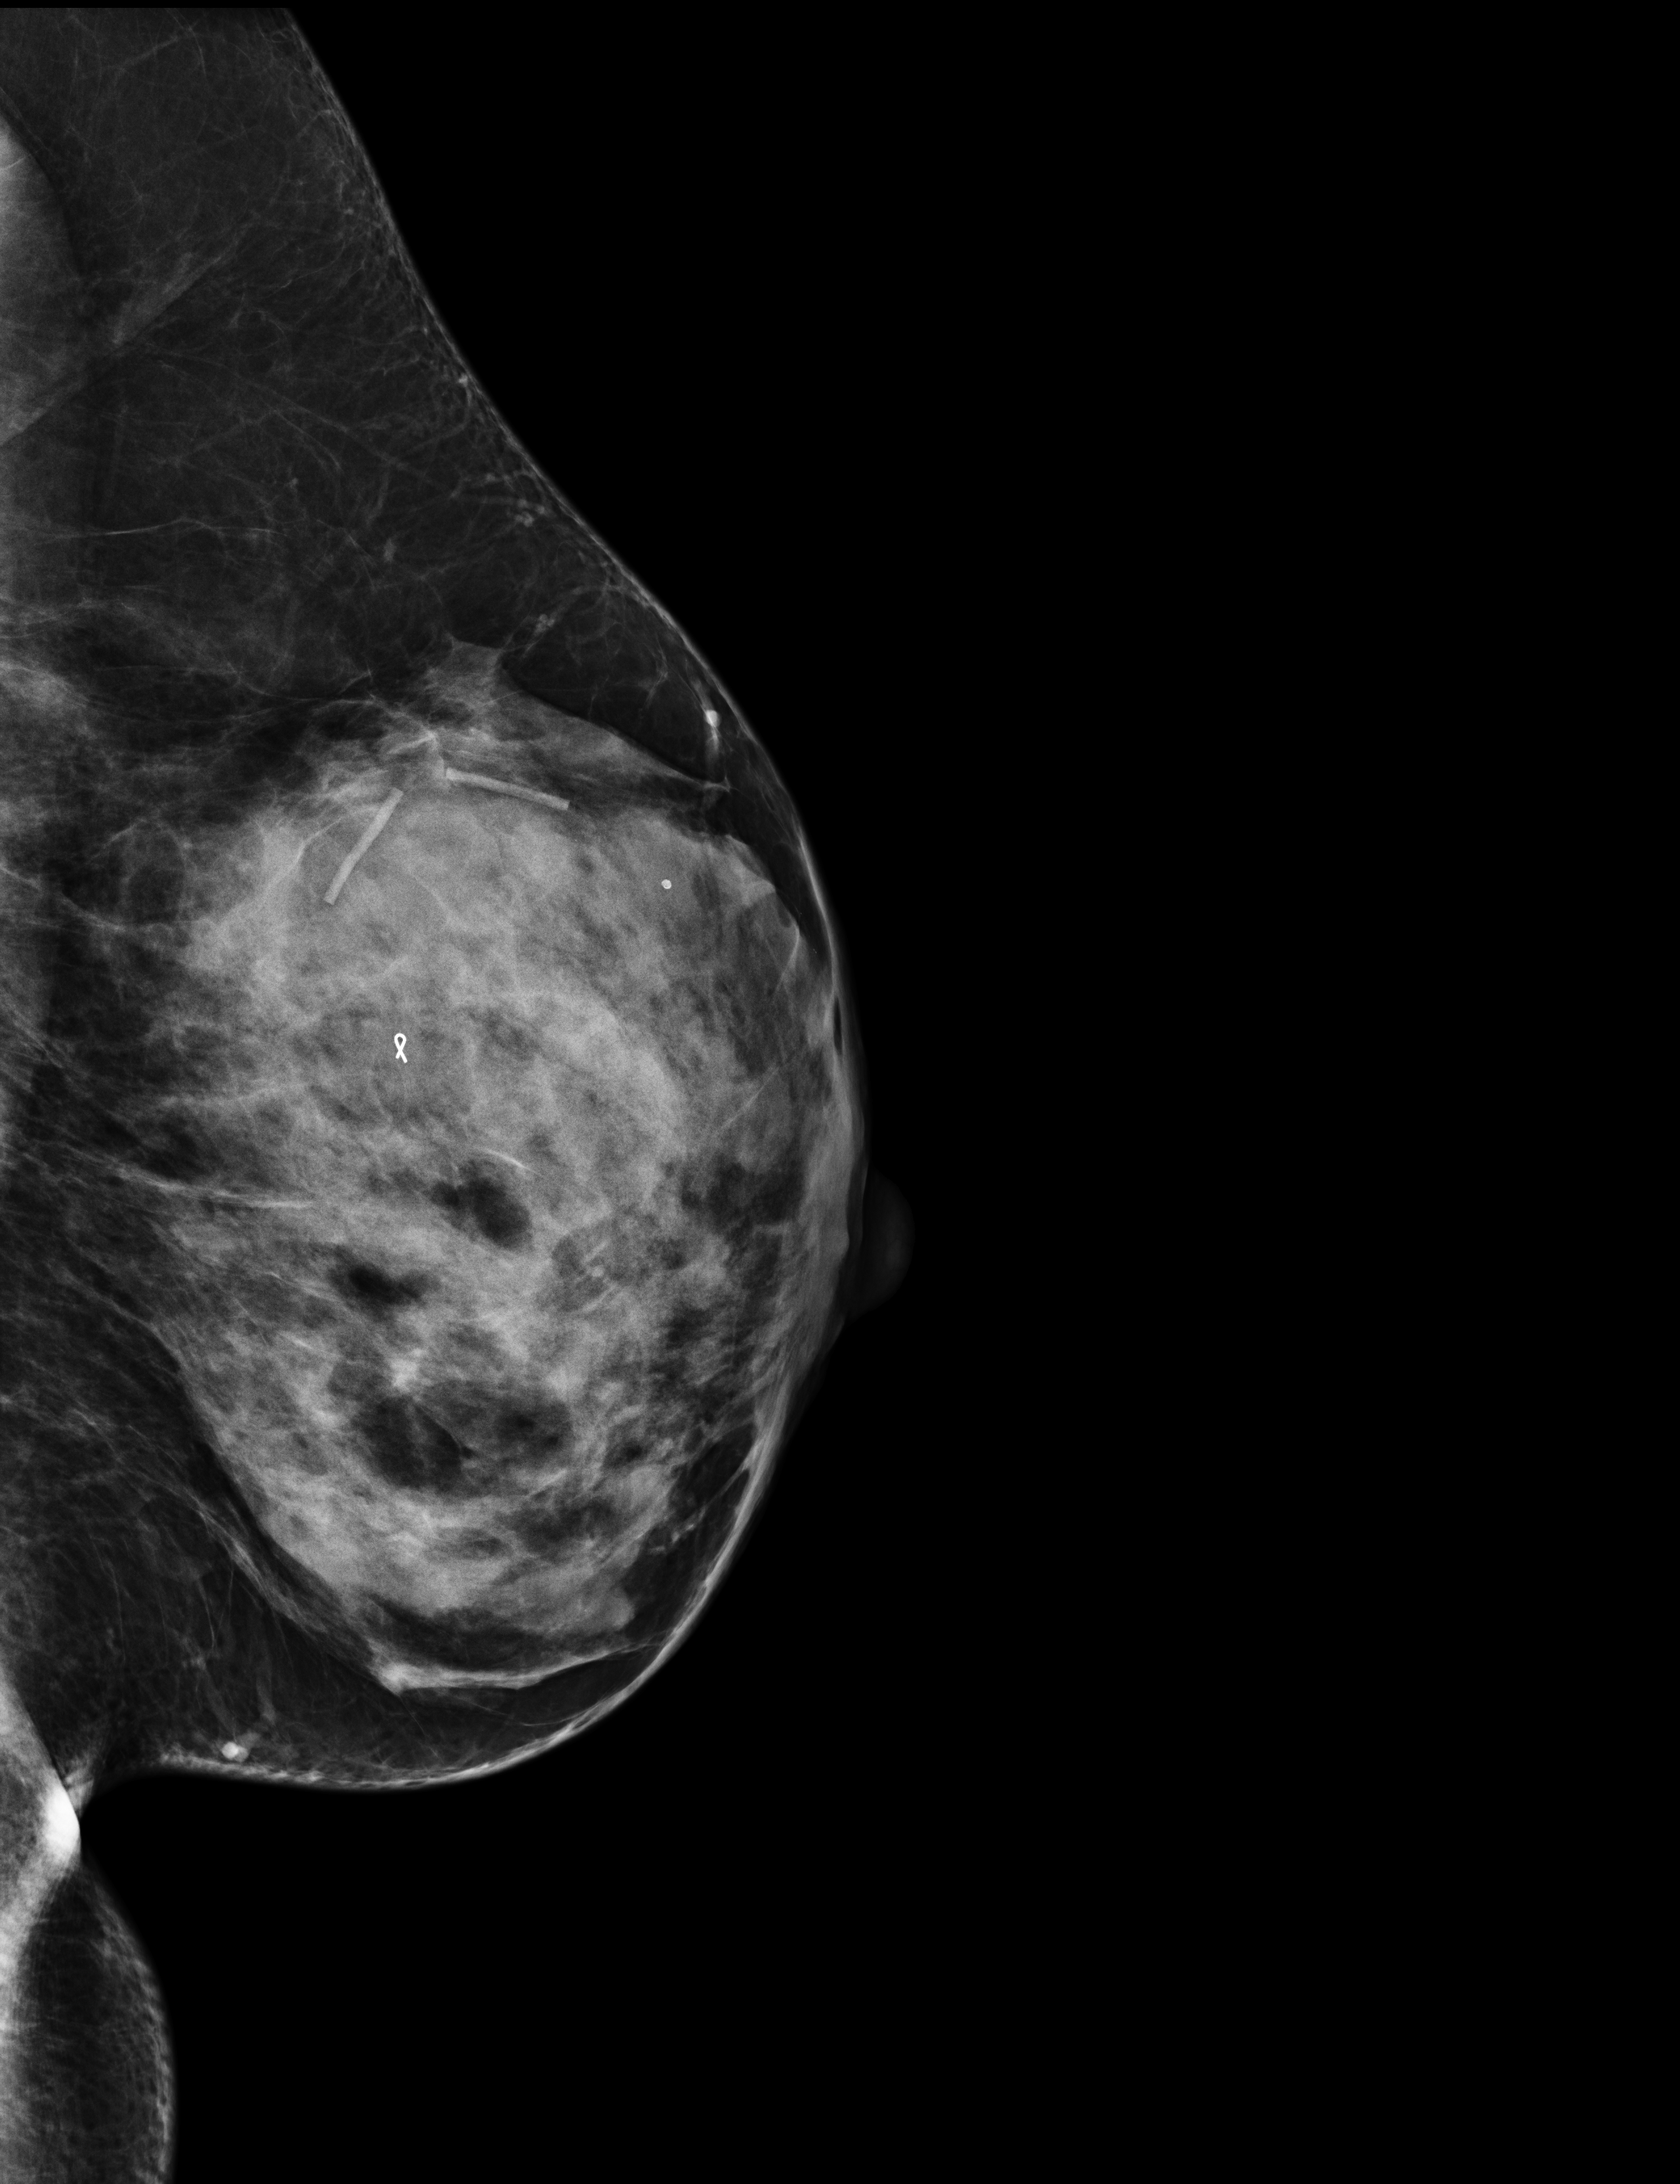
Full-field digital mammogram (FFDM), left breast, MLO view, annual screening mammography examination, compressed breast thickness 54 mm. Female patient, age 47 years.
- BI-RADS breast density category at the screening exam (both breasts, scale 1–4): 3
- final BI-RADS assessment for this screening round (tomosynthesis exam, both breasts): category 4
- recall: recalled for additional imaging after this screen